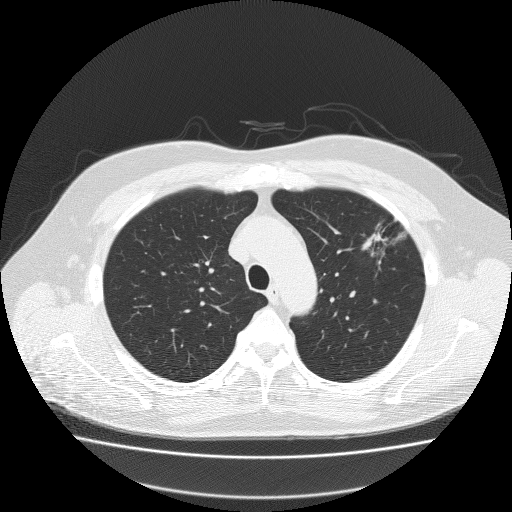
Chest CT (low-dose screening protocol), one axial image. Baseline screening round. Lung window (W 1500 / L -600 HU). 2 mm slice thickness. Slice 51 of 204 in the series. 512 × 512 image matrix. Male, age 62 years at enrolment. Former smoker at enrolment.
- Expert-annotated lung lesion, bounding box (x1, y1, x2, y2) in pixels: (351, 209, 419, 264).
- Screening reader's record for this exam (one nodule recorded; not confirmed to be the boxed lesion): non-calcified nodule or mass ≥4 mm, left upper lobe, 18 × 8 mm, spiculated (stellate) margins, soft tissue attenuation.
- Official screen result: positive, change unspecified: nodule(s) >= 4 mm or enlarging nodule(s), mass(es), or other non-specific abnormalities suspicious for lung cancer.
- Later outcome: lung cancer diagnosed 49 days after this screen — bronchiolo-alveolar adenocarcinoma, NOS, left upper lobe, well differentiated (G1), stage IA (AJCC 6th edition), 25 mm at pathology.